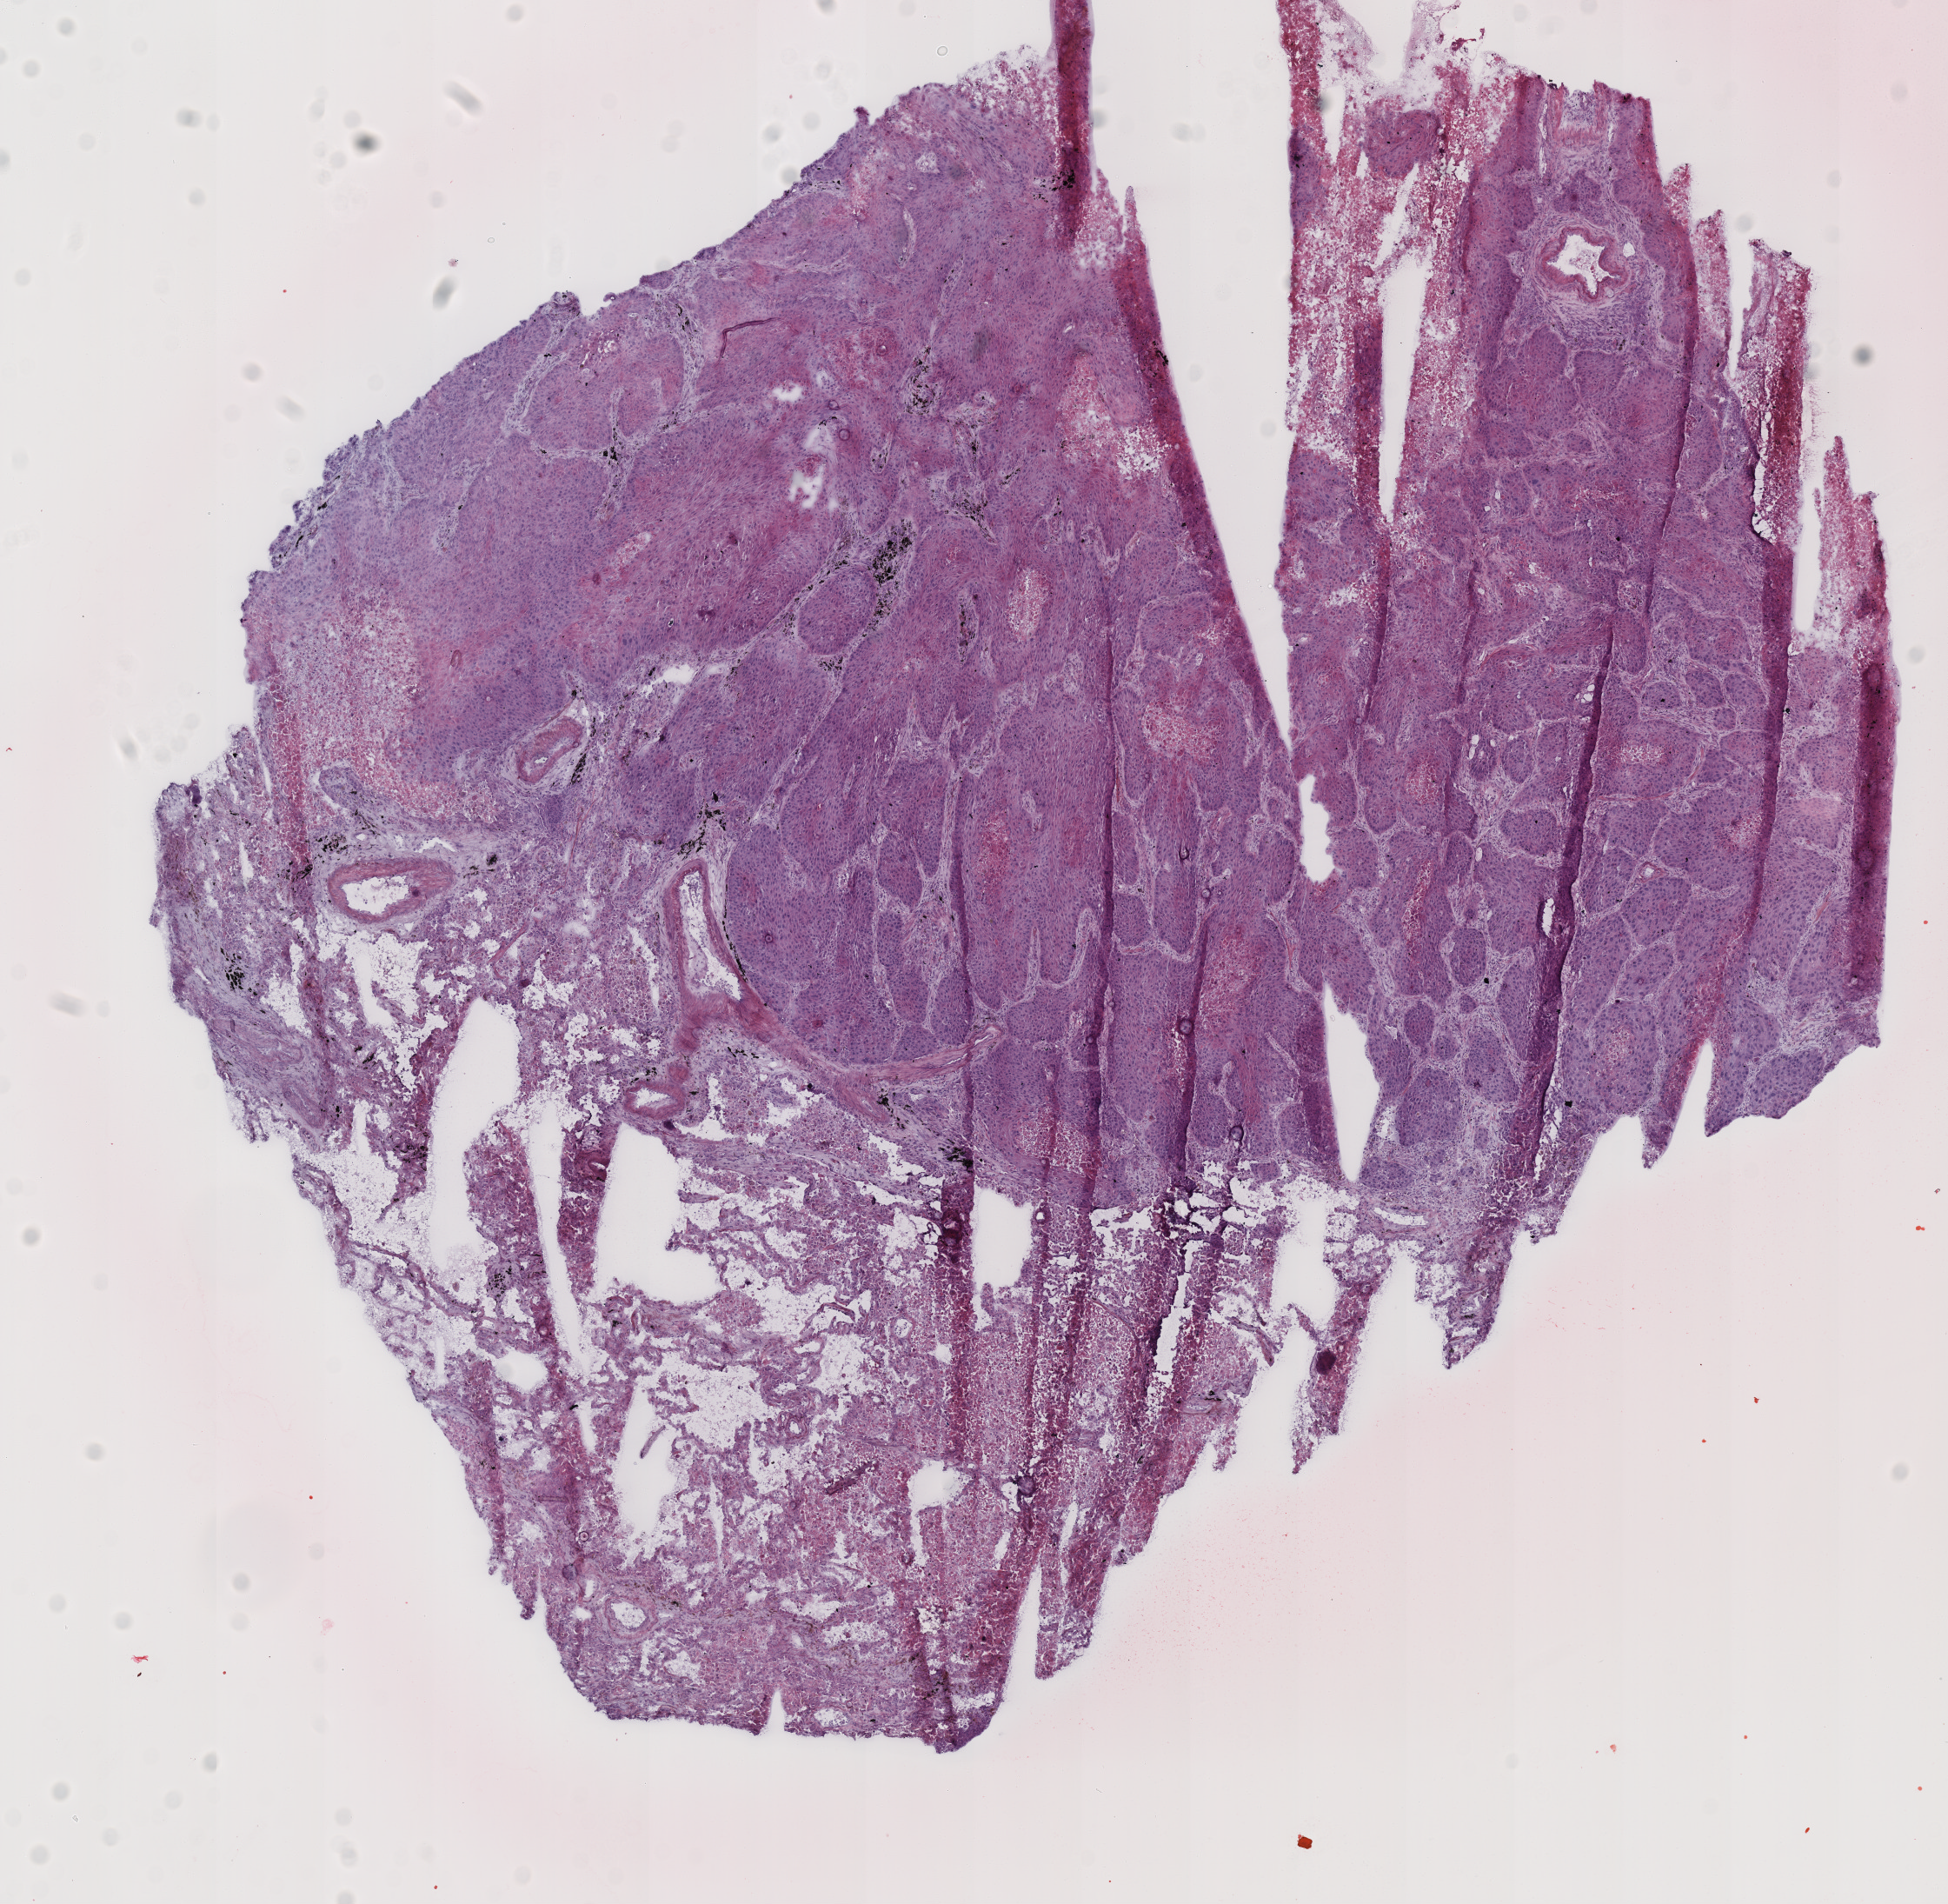
Whole-slide histology image, H&E, whole scanned area (about 8.8 x 8.6 mm) shown as a low-resolution overview; frozen section from the top of the tissue portion; lung, primary tumour sample. Patient: male, age at initial diagnosis 75 years. Composition of this section per pathologist review: tumour cells 60%, tumour nuclei 65%, normal cells 30%, stromal cells 0%, necrosis 10%. Infiltration values recorded for this section: monocyte infiltration 15%.
* AJCC pathologic stage: IV (6th edition)
* TNM: T3 NX M1
* histologic diagnosis: Squamous cell carcinoma, NOS (upper lobe, lung)